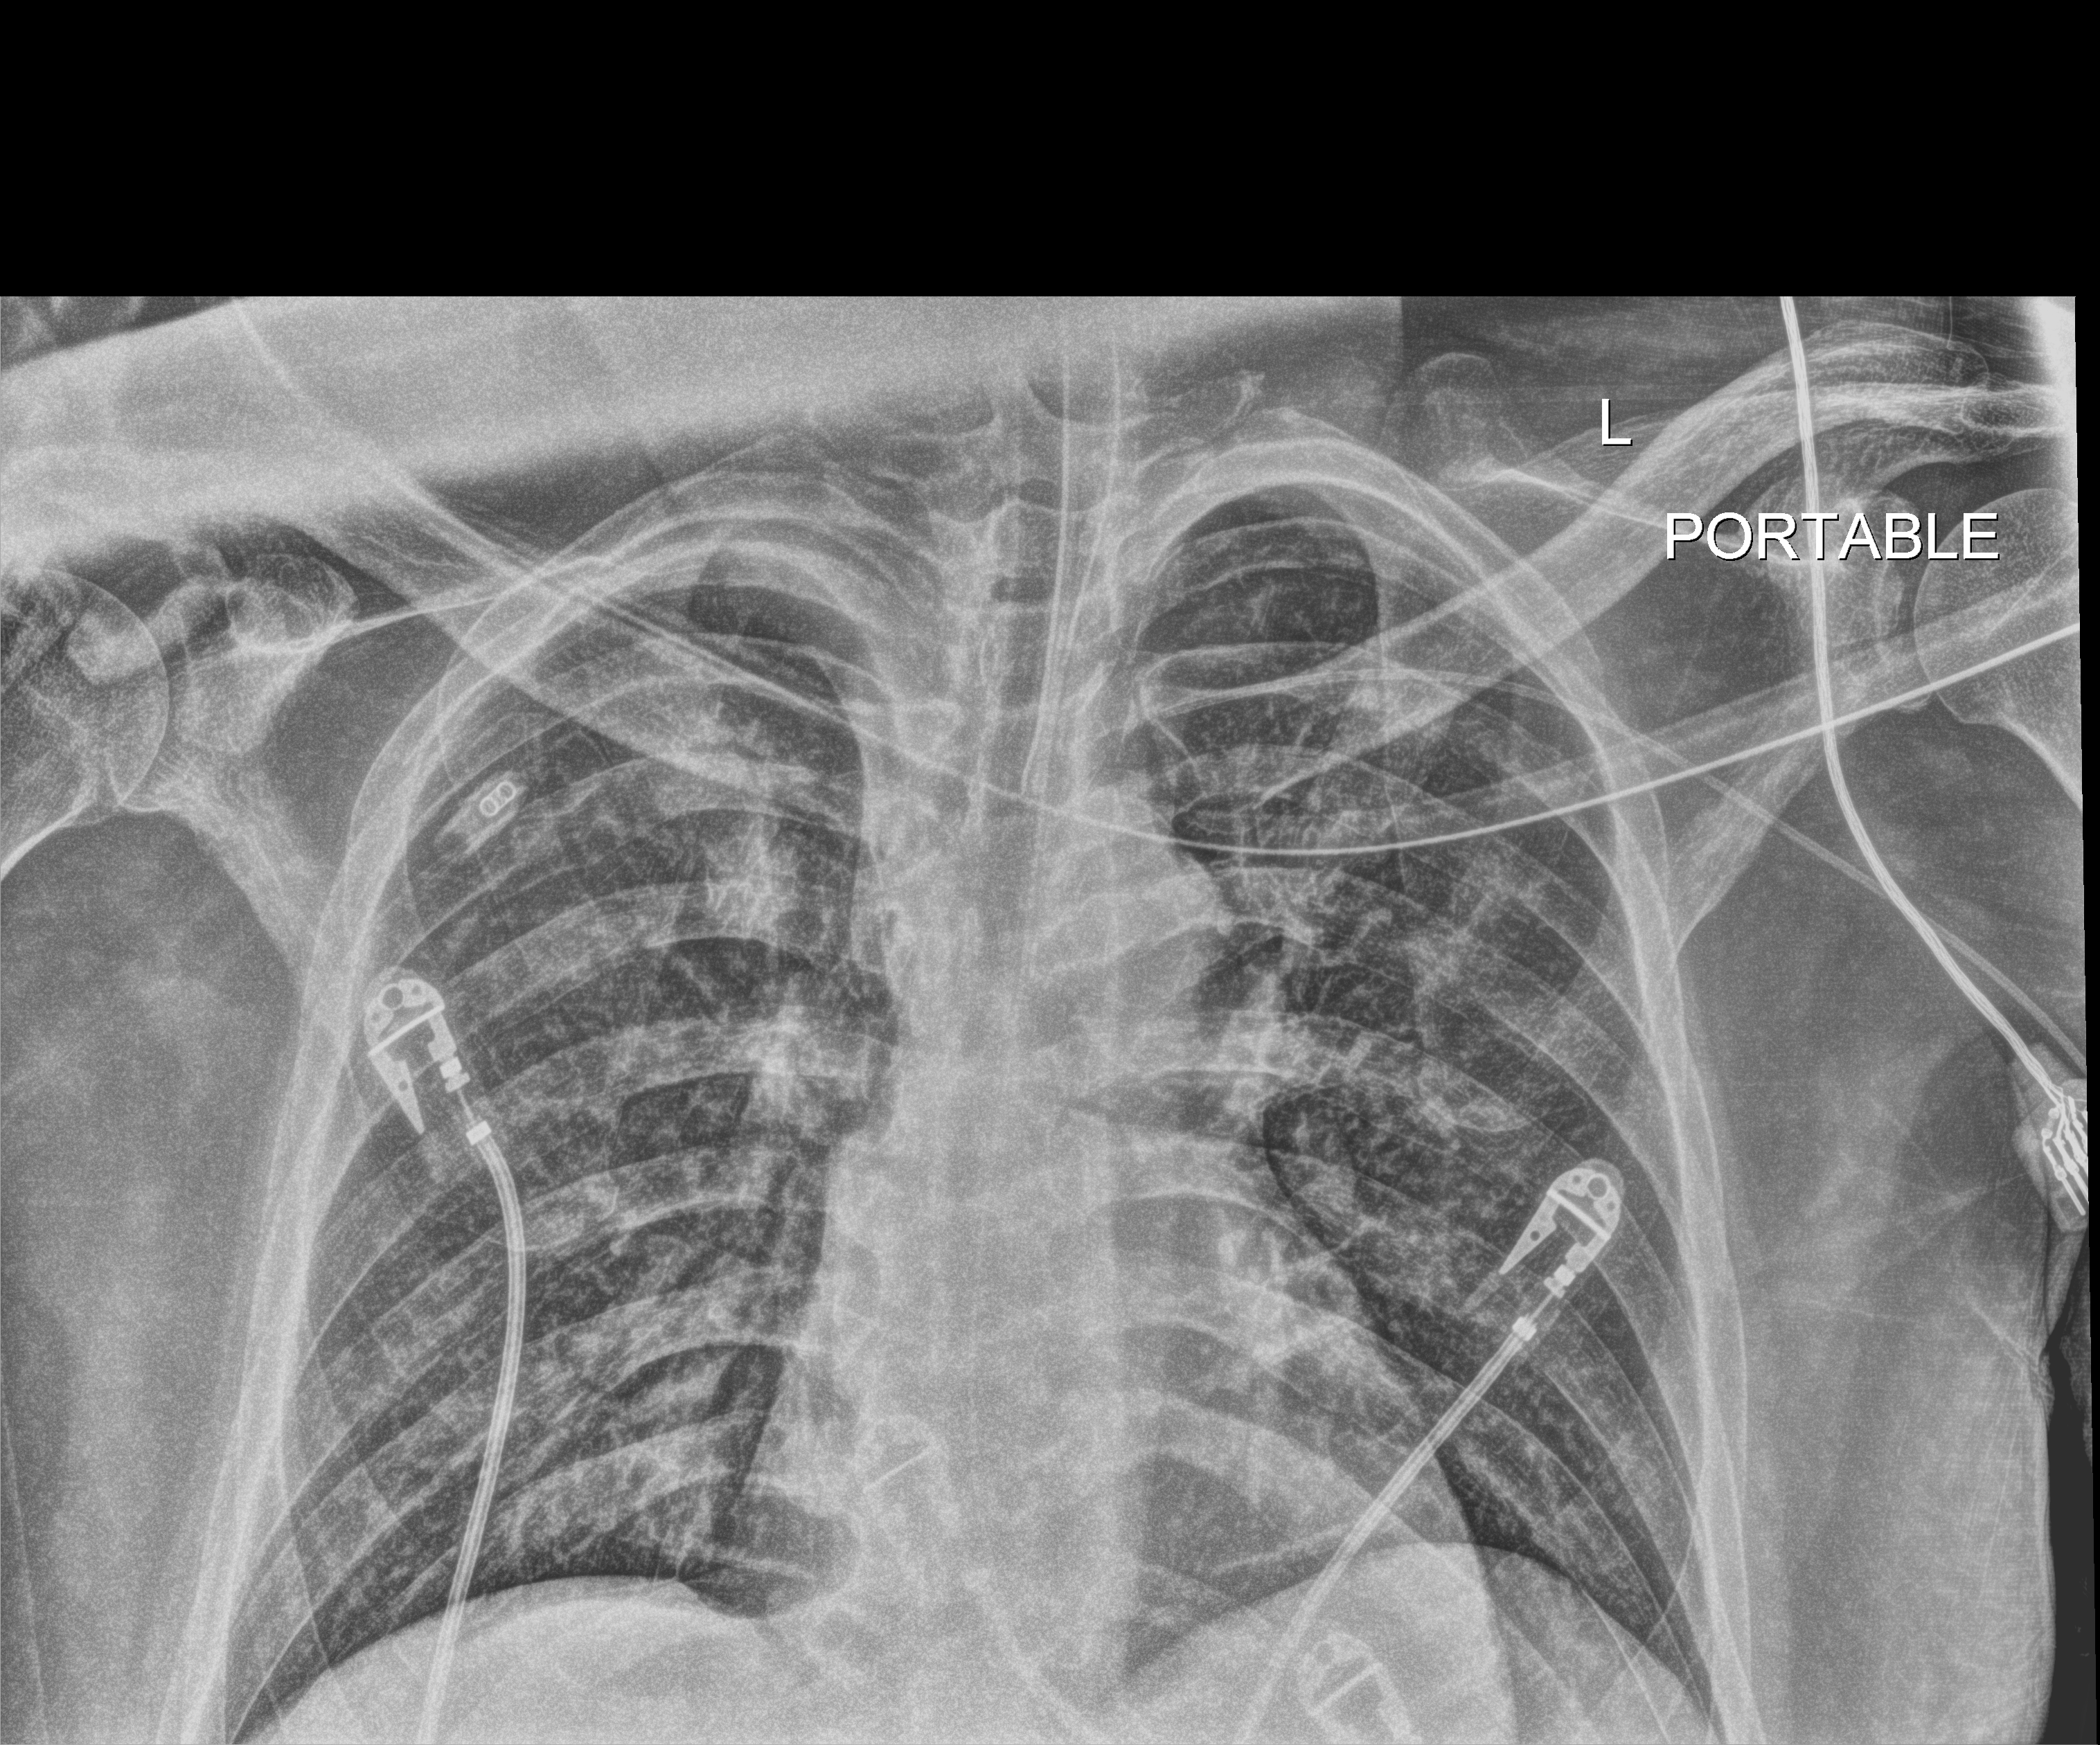
Portable chest radiograph; anteroposterior (AP) projection. Adult patient hospitalised with COVID-19, age 18–59 years.
Admission-level facts for this patient (not findings on this image; timing relative to this image not recorded):
- admitted to intensive care during this hospital stay: yes
- chronic kidney disease (admission record): no